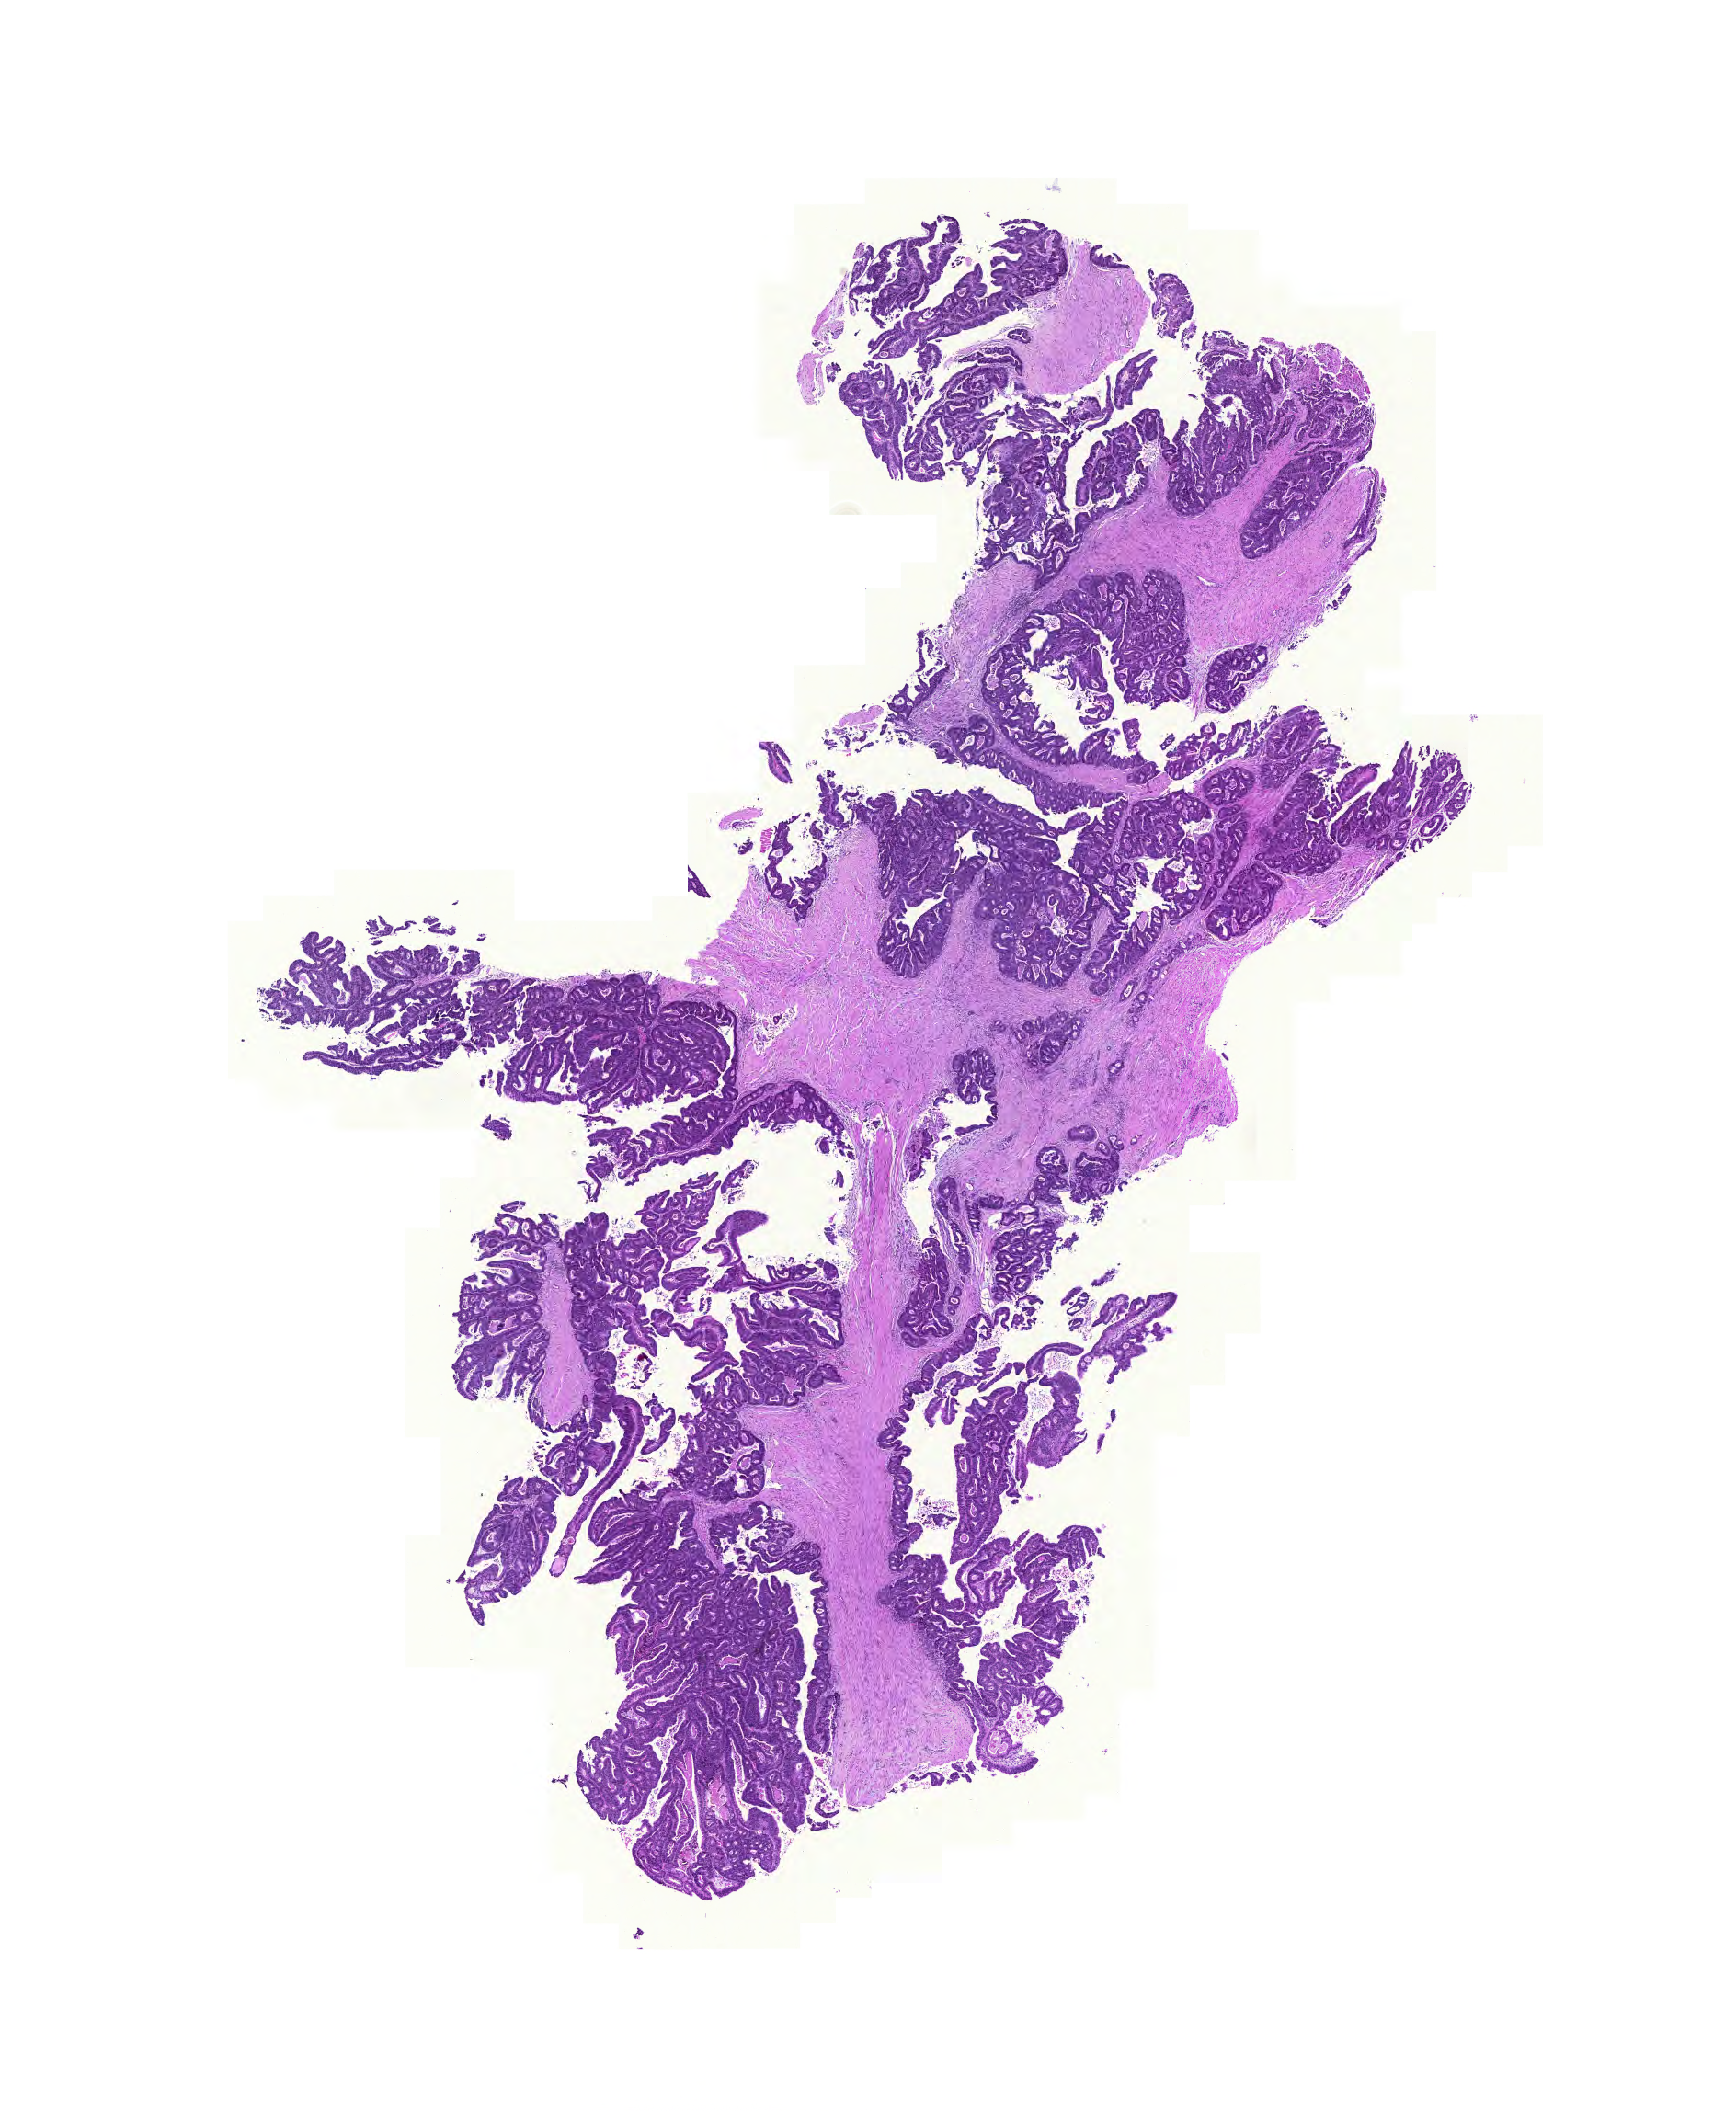
Whole-slide histology image, H&E-stained — shown as a low-resolution overview of the whole scanned area (about 14.0 x 17.1 mm), FFPE section, sample: primary tumour, colon. Female patient; age at initial diagnosis 77 years.
Pathologic diagnosis: Adenocarcinoma, NOS (sigmoid colon). AJCC pathologic stage: IV (6th edition). Lymph nodes positive (case pathology): 2 of 17 examined.